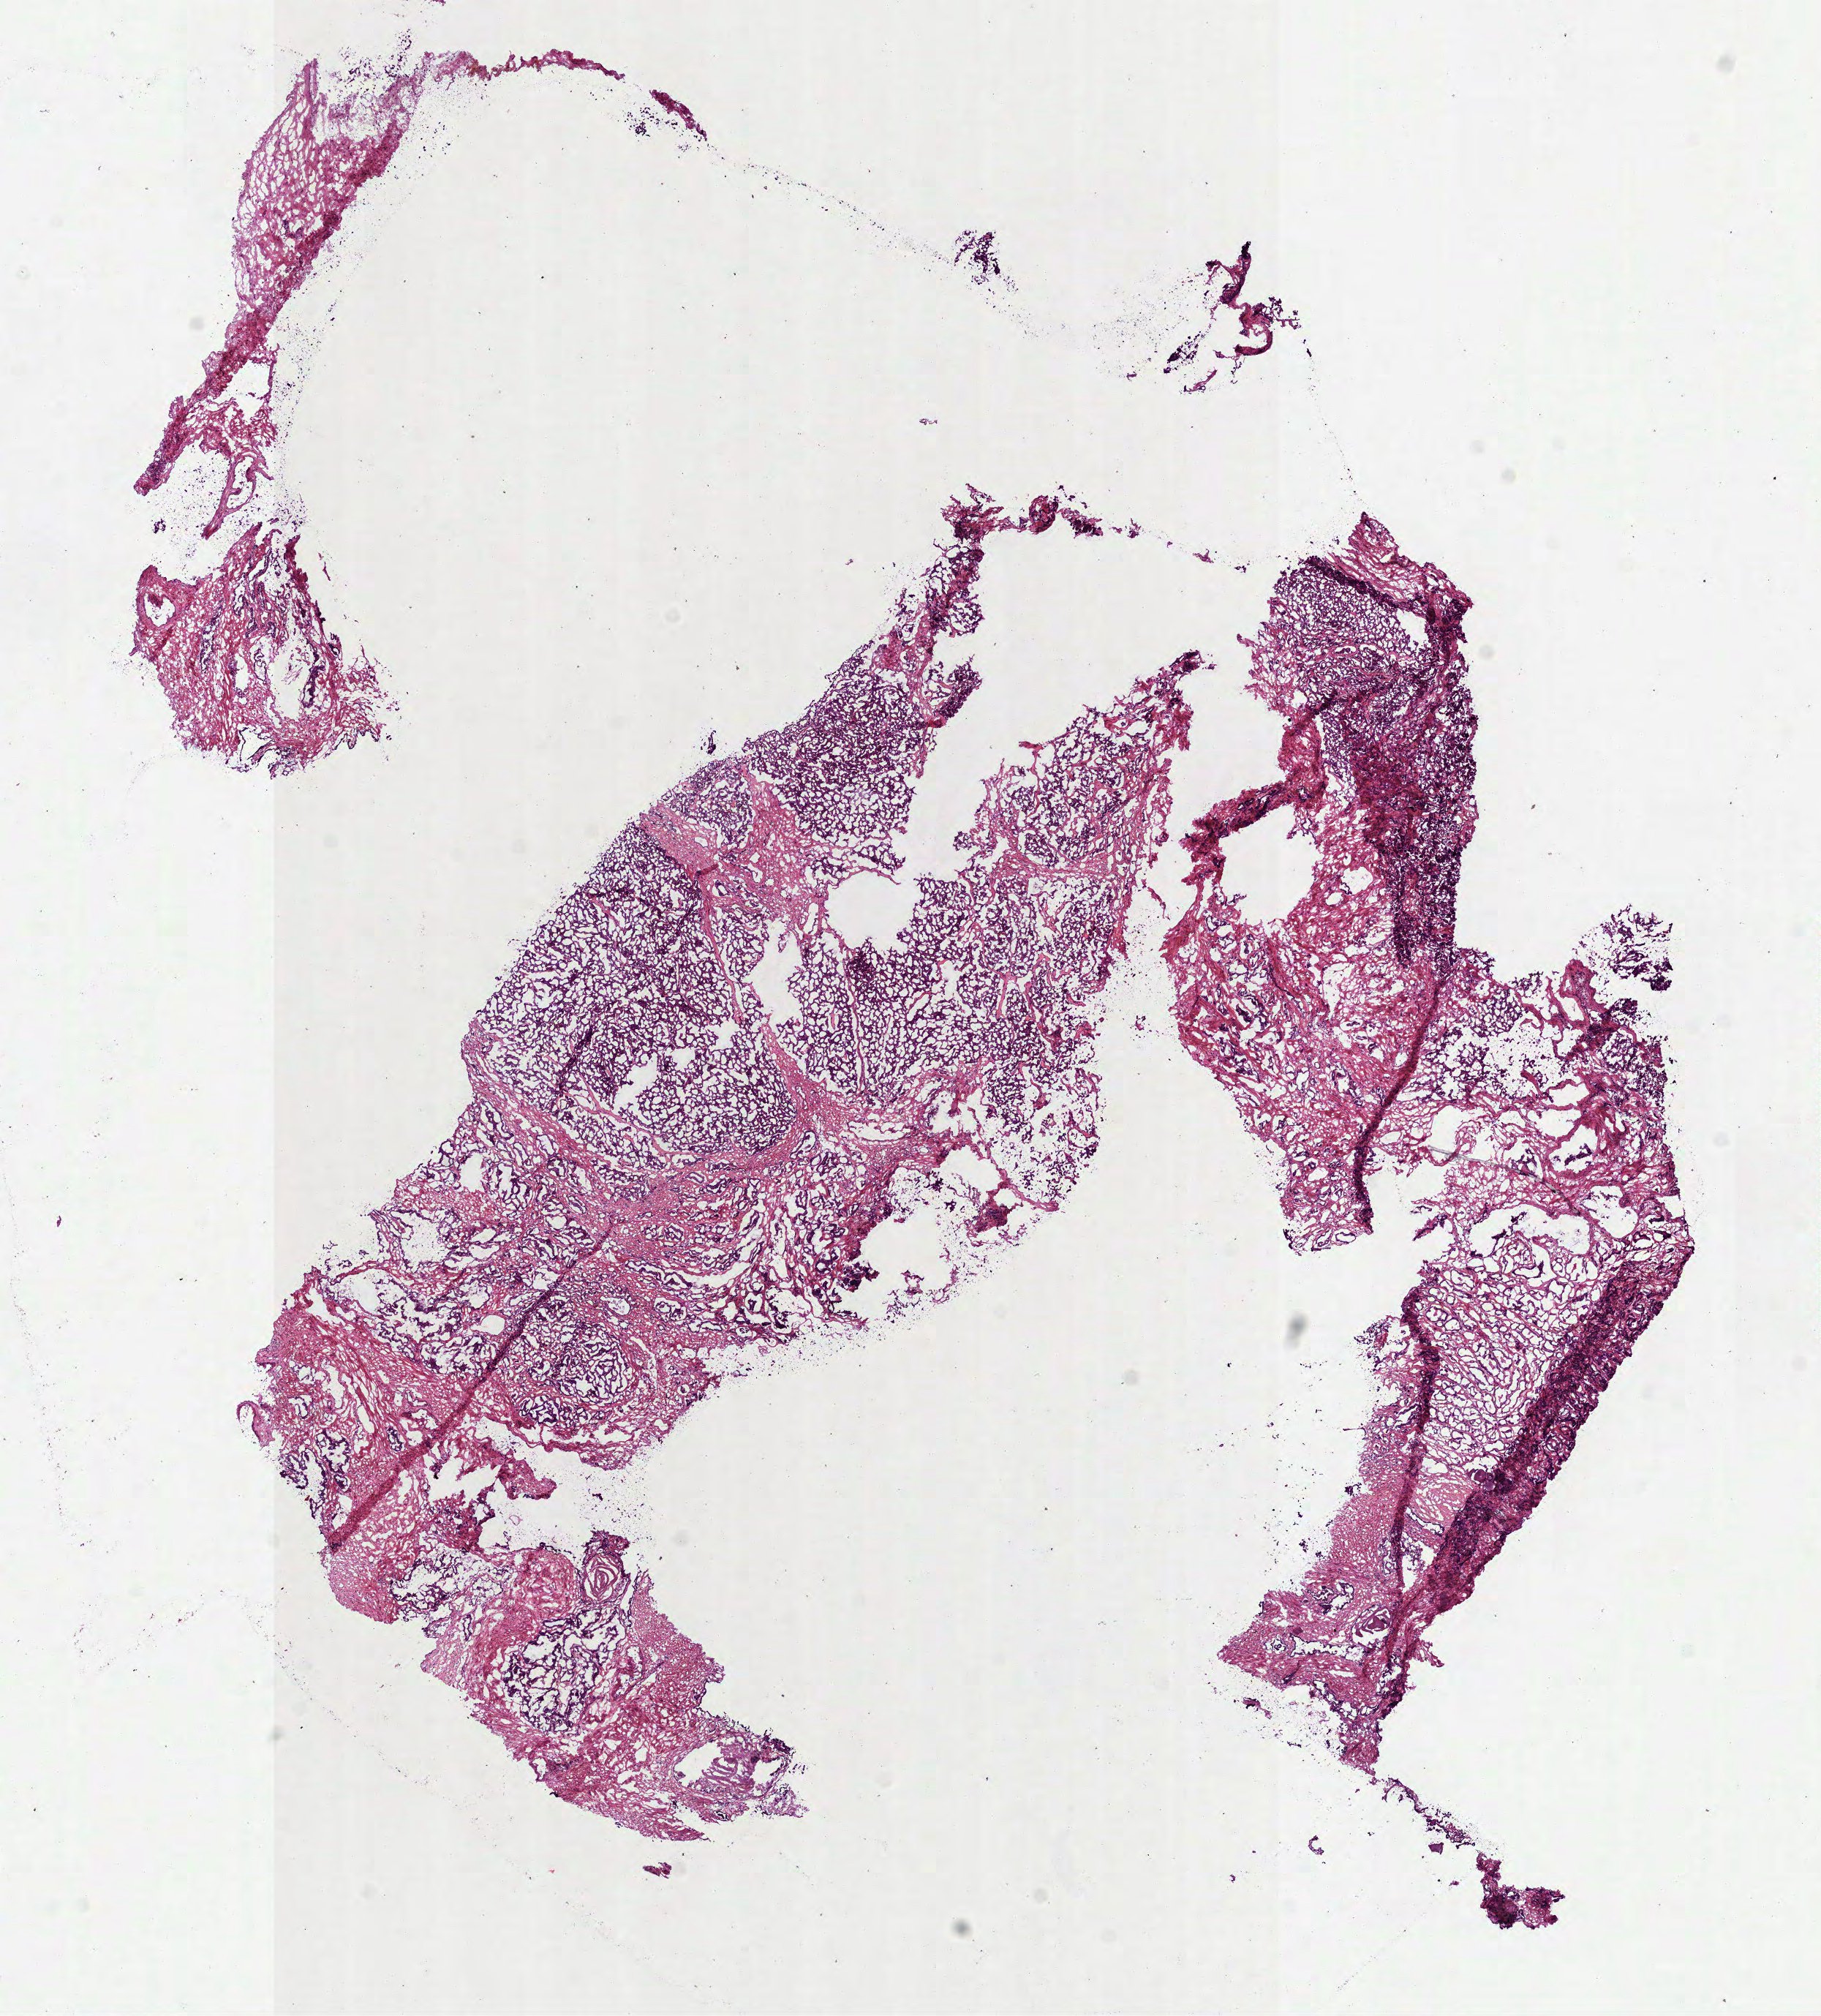
Whole-slide histology image, H&E-stained, a low-resolution overview of the entire scanned area, about 10.0 x 11.1 mm (acquisition: 40x scan), frozen section from the bottom of the tissue portion, sample: primary tumour, prostate. Male patient; age at initial diagnosis 61 years. Gleason score: 7 (4+3). Composition of this section per pathologist review: tumour cells 75%, tumour nuclei 70%, normal cells 5%, stromal cells 20%, necrosis 0%. Infiltration values recorded for this section: lymphocyte infiltration 2%, monocyte infiltration 0%, neutrophil infiltration 0%.
Pathologic diagnosis: Acinar cell carcinoma (prostate gland). Lymph nodes positive (case pathology): 0 of 15 examined. Laterality: bilateral.